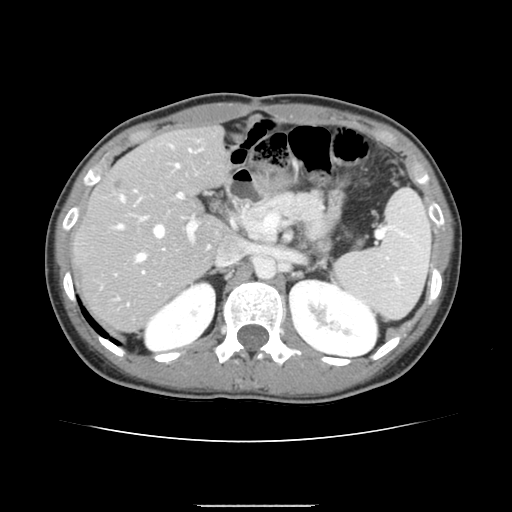
Contrast-enhanced abdominal CT, one axial slice; position 90 of 150 along the scan axis; 120 kVp; intravenous contrast given; soft-tissue window (W 400 / L 40 HU); 512 × 512 image matrix, field of view 324 × 324 mm. Female patient, age 32 years. Case-level facts recorded for this patient, not image findings: diagnosis: colorectal cancer liver metastases, imaged before liver resection; multiple liver metastases: yes; largest metastasis: 0.7 cm; disease in both lobes: no.
Structures marked on this image (manually delineated by an expert):
- hepatic veins: bounding box [x1, y1, x2, y2] px = [118, 149, 191, 261]
- liver: [74, 128, 228, 332]
- planned liver remnant (the part of the liver to remain after resection): [74, 128, 228, 276]
- portal vein (with intrahepatic branches): [134, 190, 233, 273]
- liver metastasis: [116, 182, 120, 189]